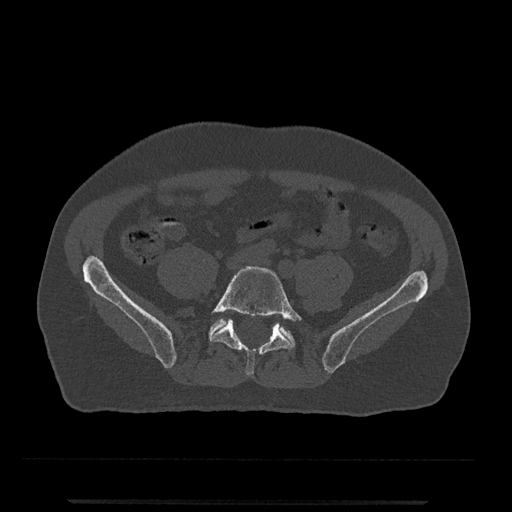
CT including the spine, one axial slice; slice 66 of 797 in the series (ordered by position); reconstruction kernel Br40s/3; bone window (W 1800 / L 400 HU); 0.5 mm slice thickness; 512 × 512 image matrix, field of view 419 × 419 mm. Patient: male, 63 years. Case-level facts recorded for this patient, not image findings: primary cancer: prostate.
Annotated regions visible in this slice (semi-automatically segmented with operator editing):
- L5 vertebra: box from (x=211, y=266) to (x=302, y=377) px